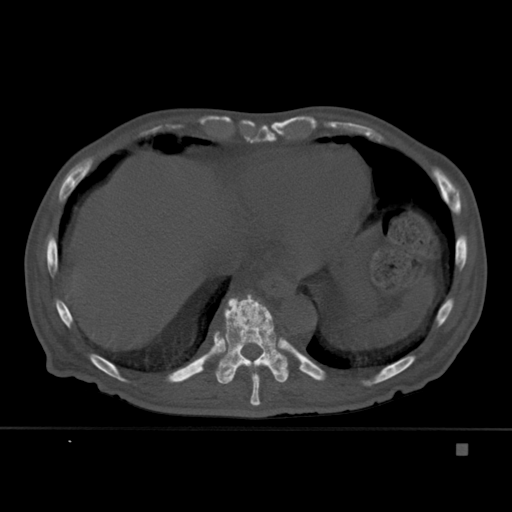
CT including the spine, one axial slice. Slice 236 of 451 in the series (ordered by position). Bone window (W 1800 / L 400 HU). 1.5 mm slice thickness. 512 × 512 image matrix, field of view 378 × 378 mm. Male patient, age 75 years. From the clinical record (not read from this slice): primary cancer: prostate.
Annotated regions visible in this slice (semi-automatic segmentation, software-assisted and operator-edited):
- T10 vertebra: bounding box <214,294,289,384> (left, top, right, bottom; pixels)
- T9 vertebra: <236,370,261,406>